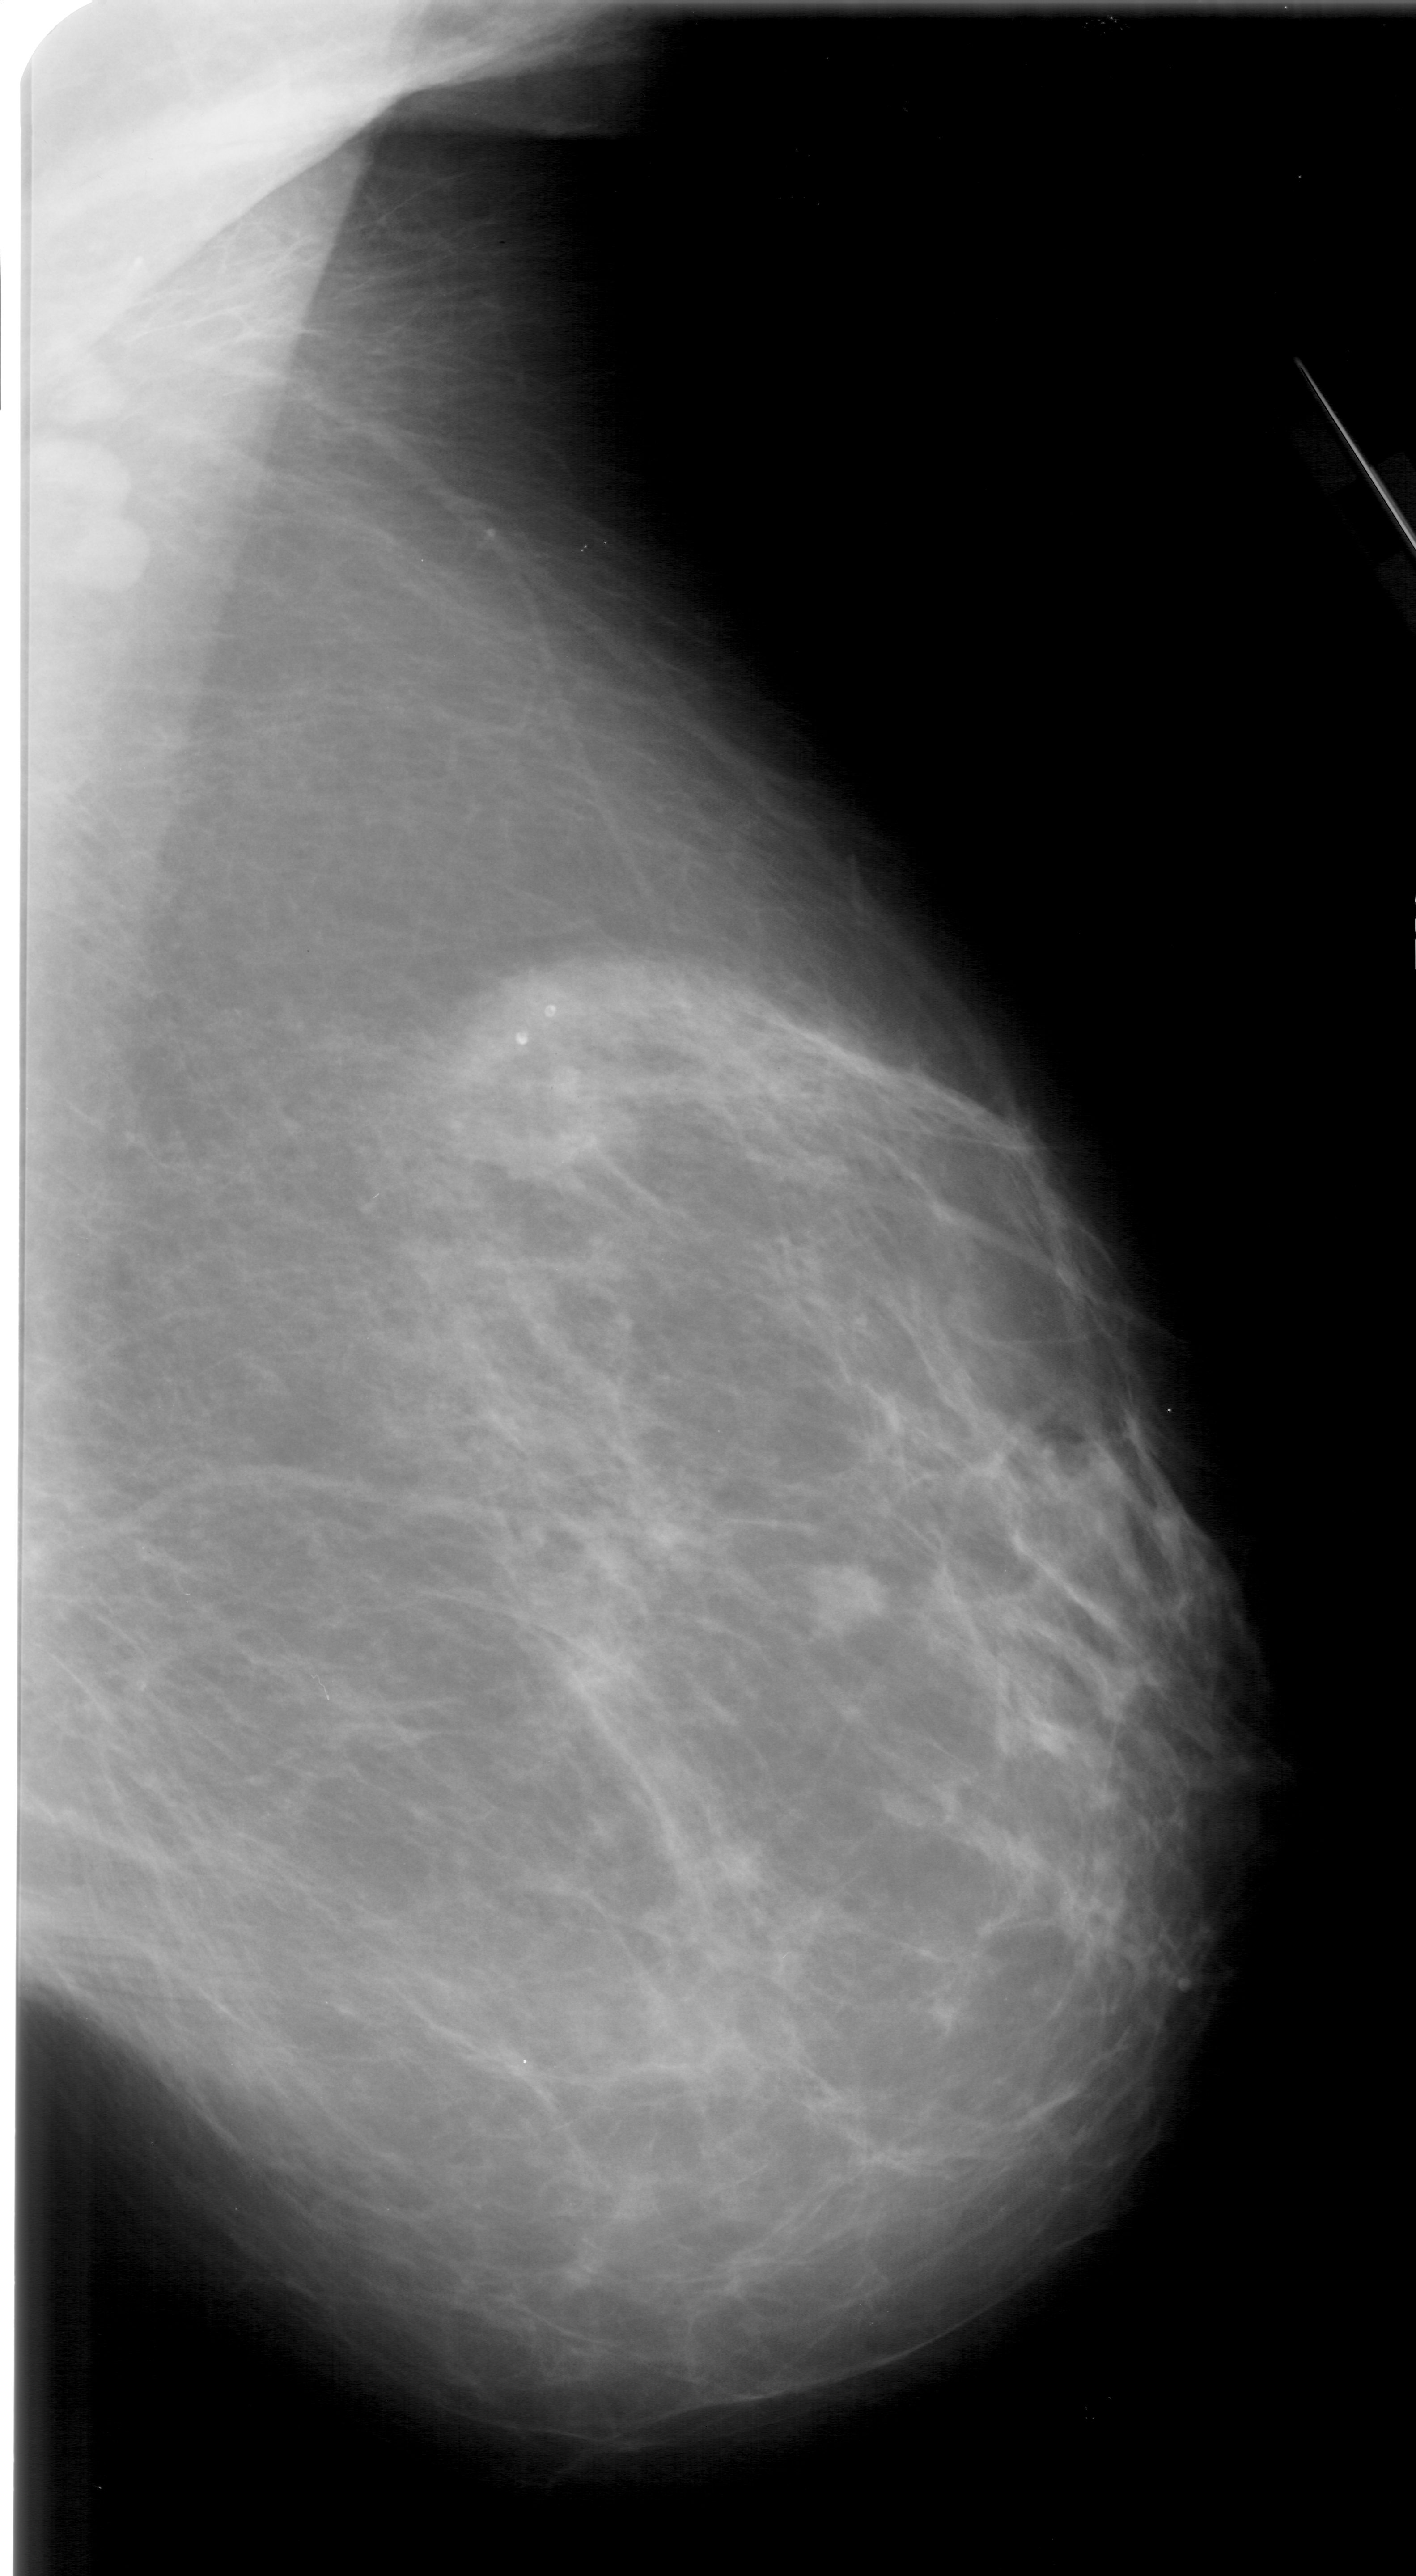
Scanned film-screen mammogram; right breast; mediolateral oblique (MLO) view; breast composition: scattered fibroglandular densities (BI-RADS density category 2 of 4); 1416 × 2576 image matrix.
Expert-marked regions of interest on this film, with their recorded descriptors:
- mass, shape irregular, margins ill defined; BI-RADS assessment category 5; subtlety rating 3 on a 1 (subtle) to 5 (obvious) scale; pathology result (as recorded, not read from the image): malignant: bounding box <802,1555,895,1629> (left, top, right, bottom; pixels)